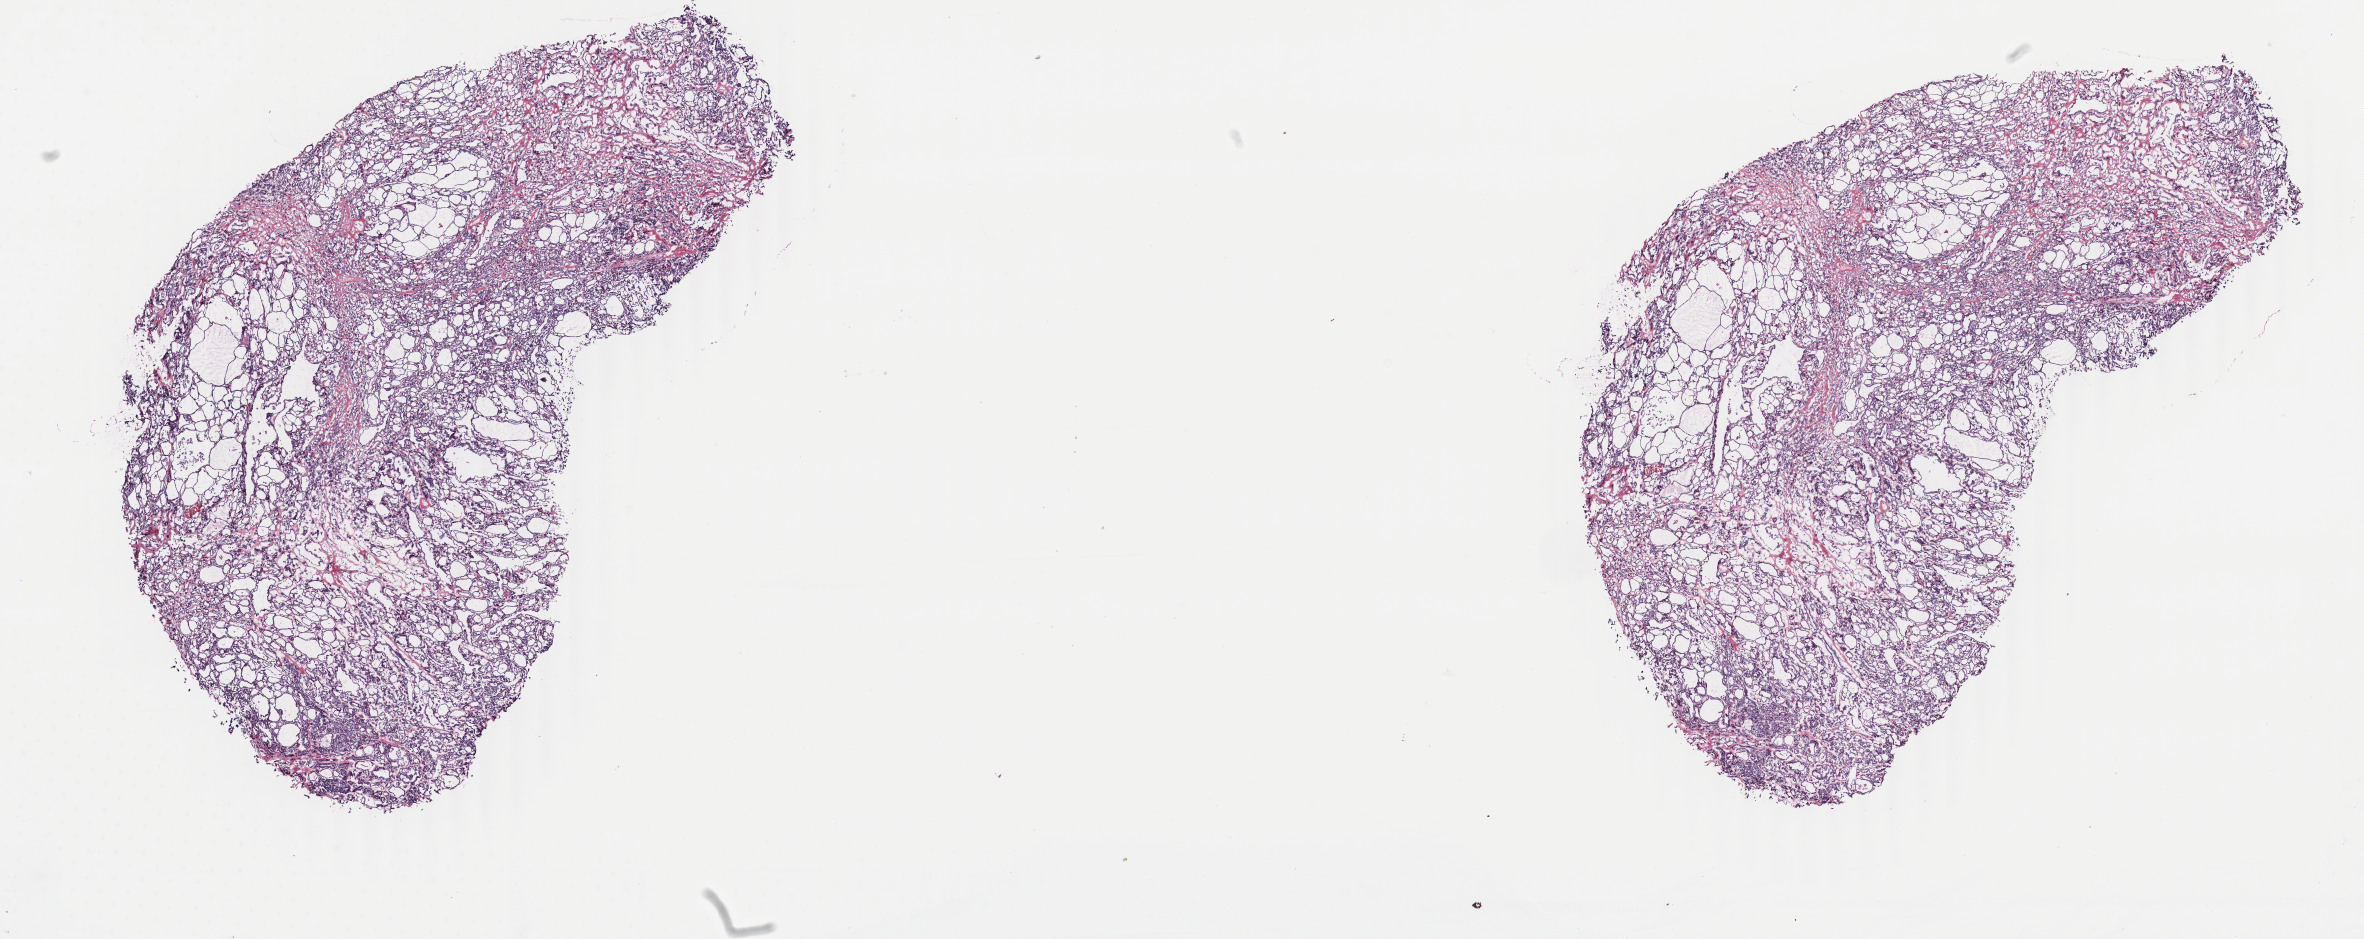
Hematoxylin and eosin (H&E) stained whole-slide image — a low-resolution overview of the entire scanned area, about 18.8 x 7.5 mm (from a 40x scan), frozen section from the top of the tissue portion, sample: primary tumour, thyroid. Female, age 26 years at initial diagnosis. Slide review estimates, as recorded: tumour cells 95%, tumour nuclei 80%, normal cells 0%, stromal cells 5%, necrosis 0%. Inflammatory infiltration, as recorded: lymphocyte infiltration 2%, monocyte infiltration 1%, neutrophil infiltration 0%.
* histologic diagnosis: Papillary carcinoma, follicular variant
* lymph nodes positive (case pathology): 0 of 2 examined
* AJCC pathologic stage: I (7th edition)